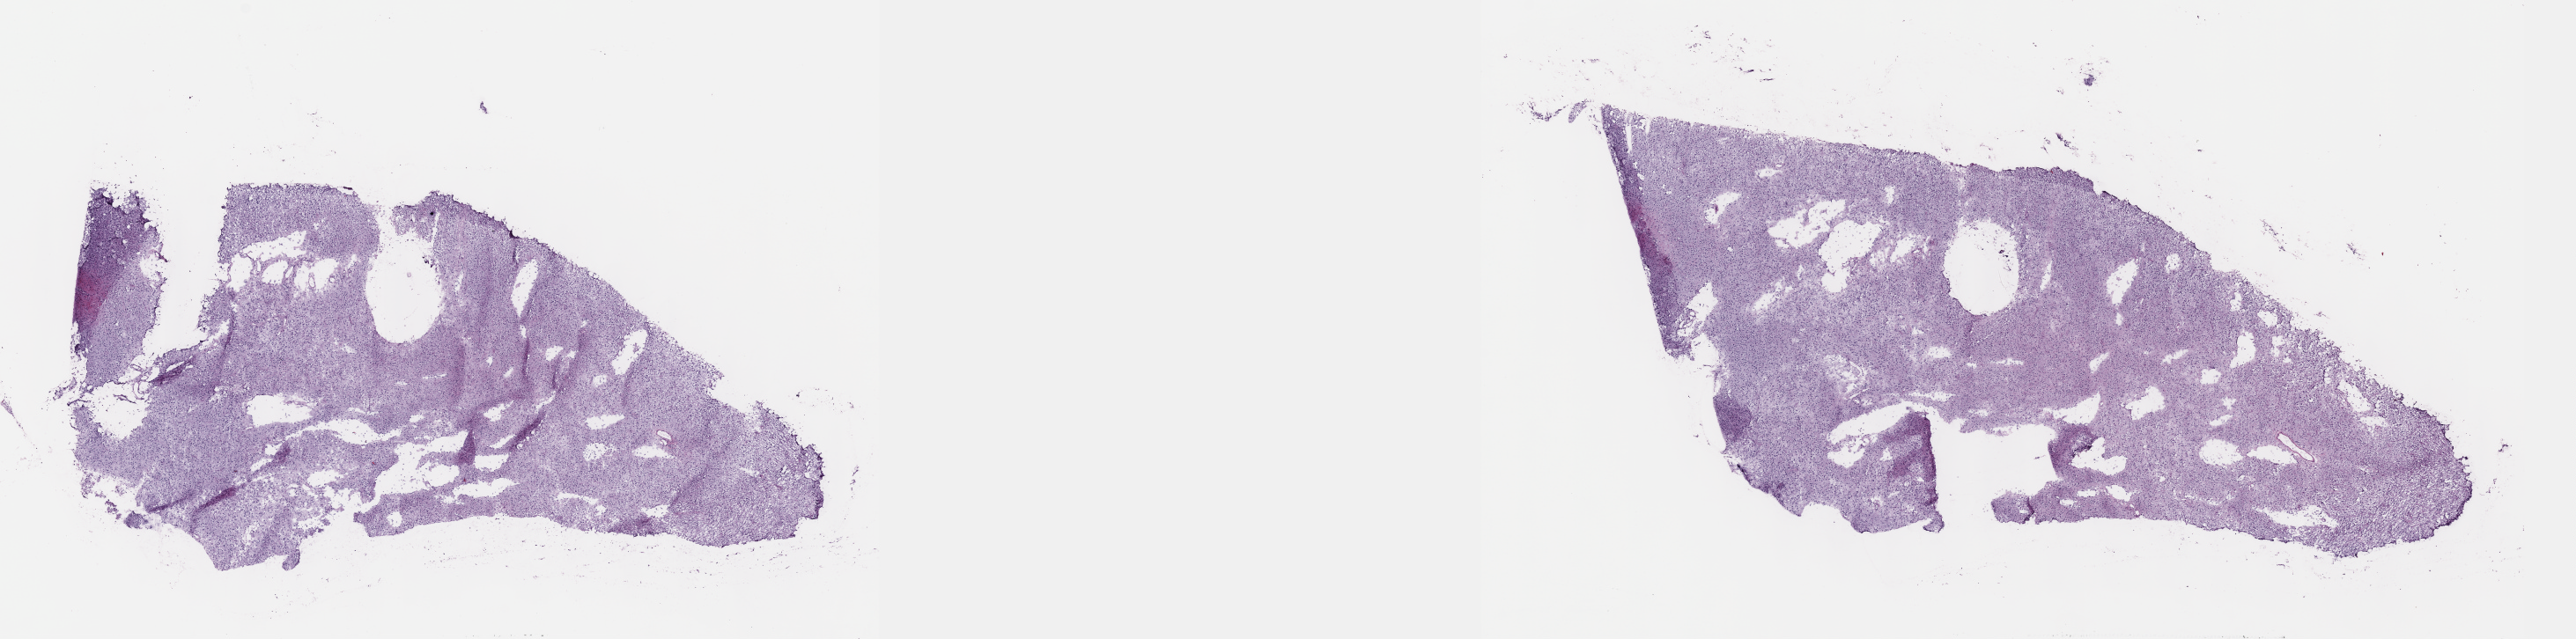
H&E whole-slide image — shown as a low-resolution overview of the whole scanned area (about 23.6 x 5.9 mm, slide scanned at 40x), frozen section from the top of the tissue portion, brain, primary tumour sample. Patient: male, age at initial diagnosis 29 years. Histologic grade: G2 (moderately differentiated). Slide review estimates, as recorded: tumour cells 50%, tumour nuclei 90%, normal cells 10%, stromal cells 40%, necrosis 0%. Infiltration values recorded for this section: lymphocyte infiltration 0%, monocyte infiltration 0%, neutrophil infiltration 0%.
Pathologic diagnosis: Mixed glioma (cerebrum).